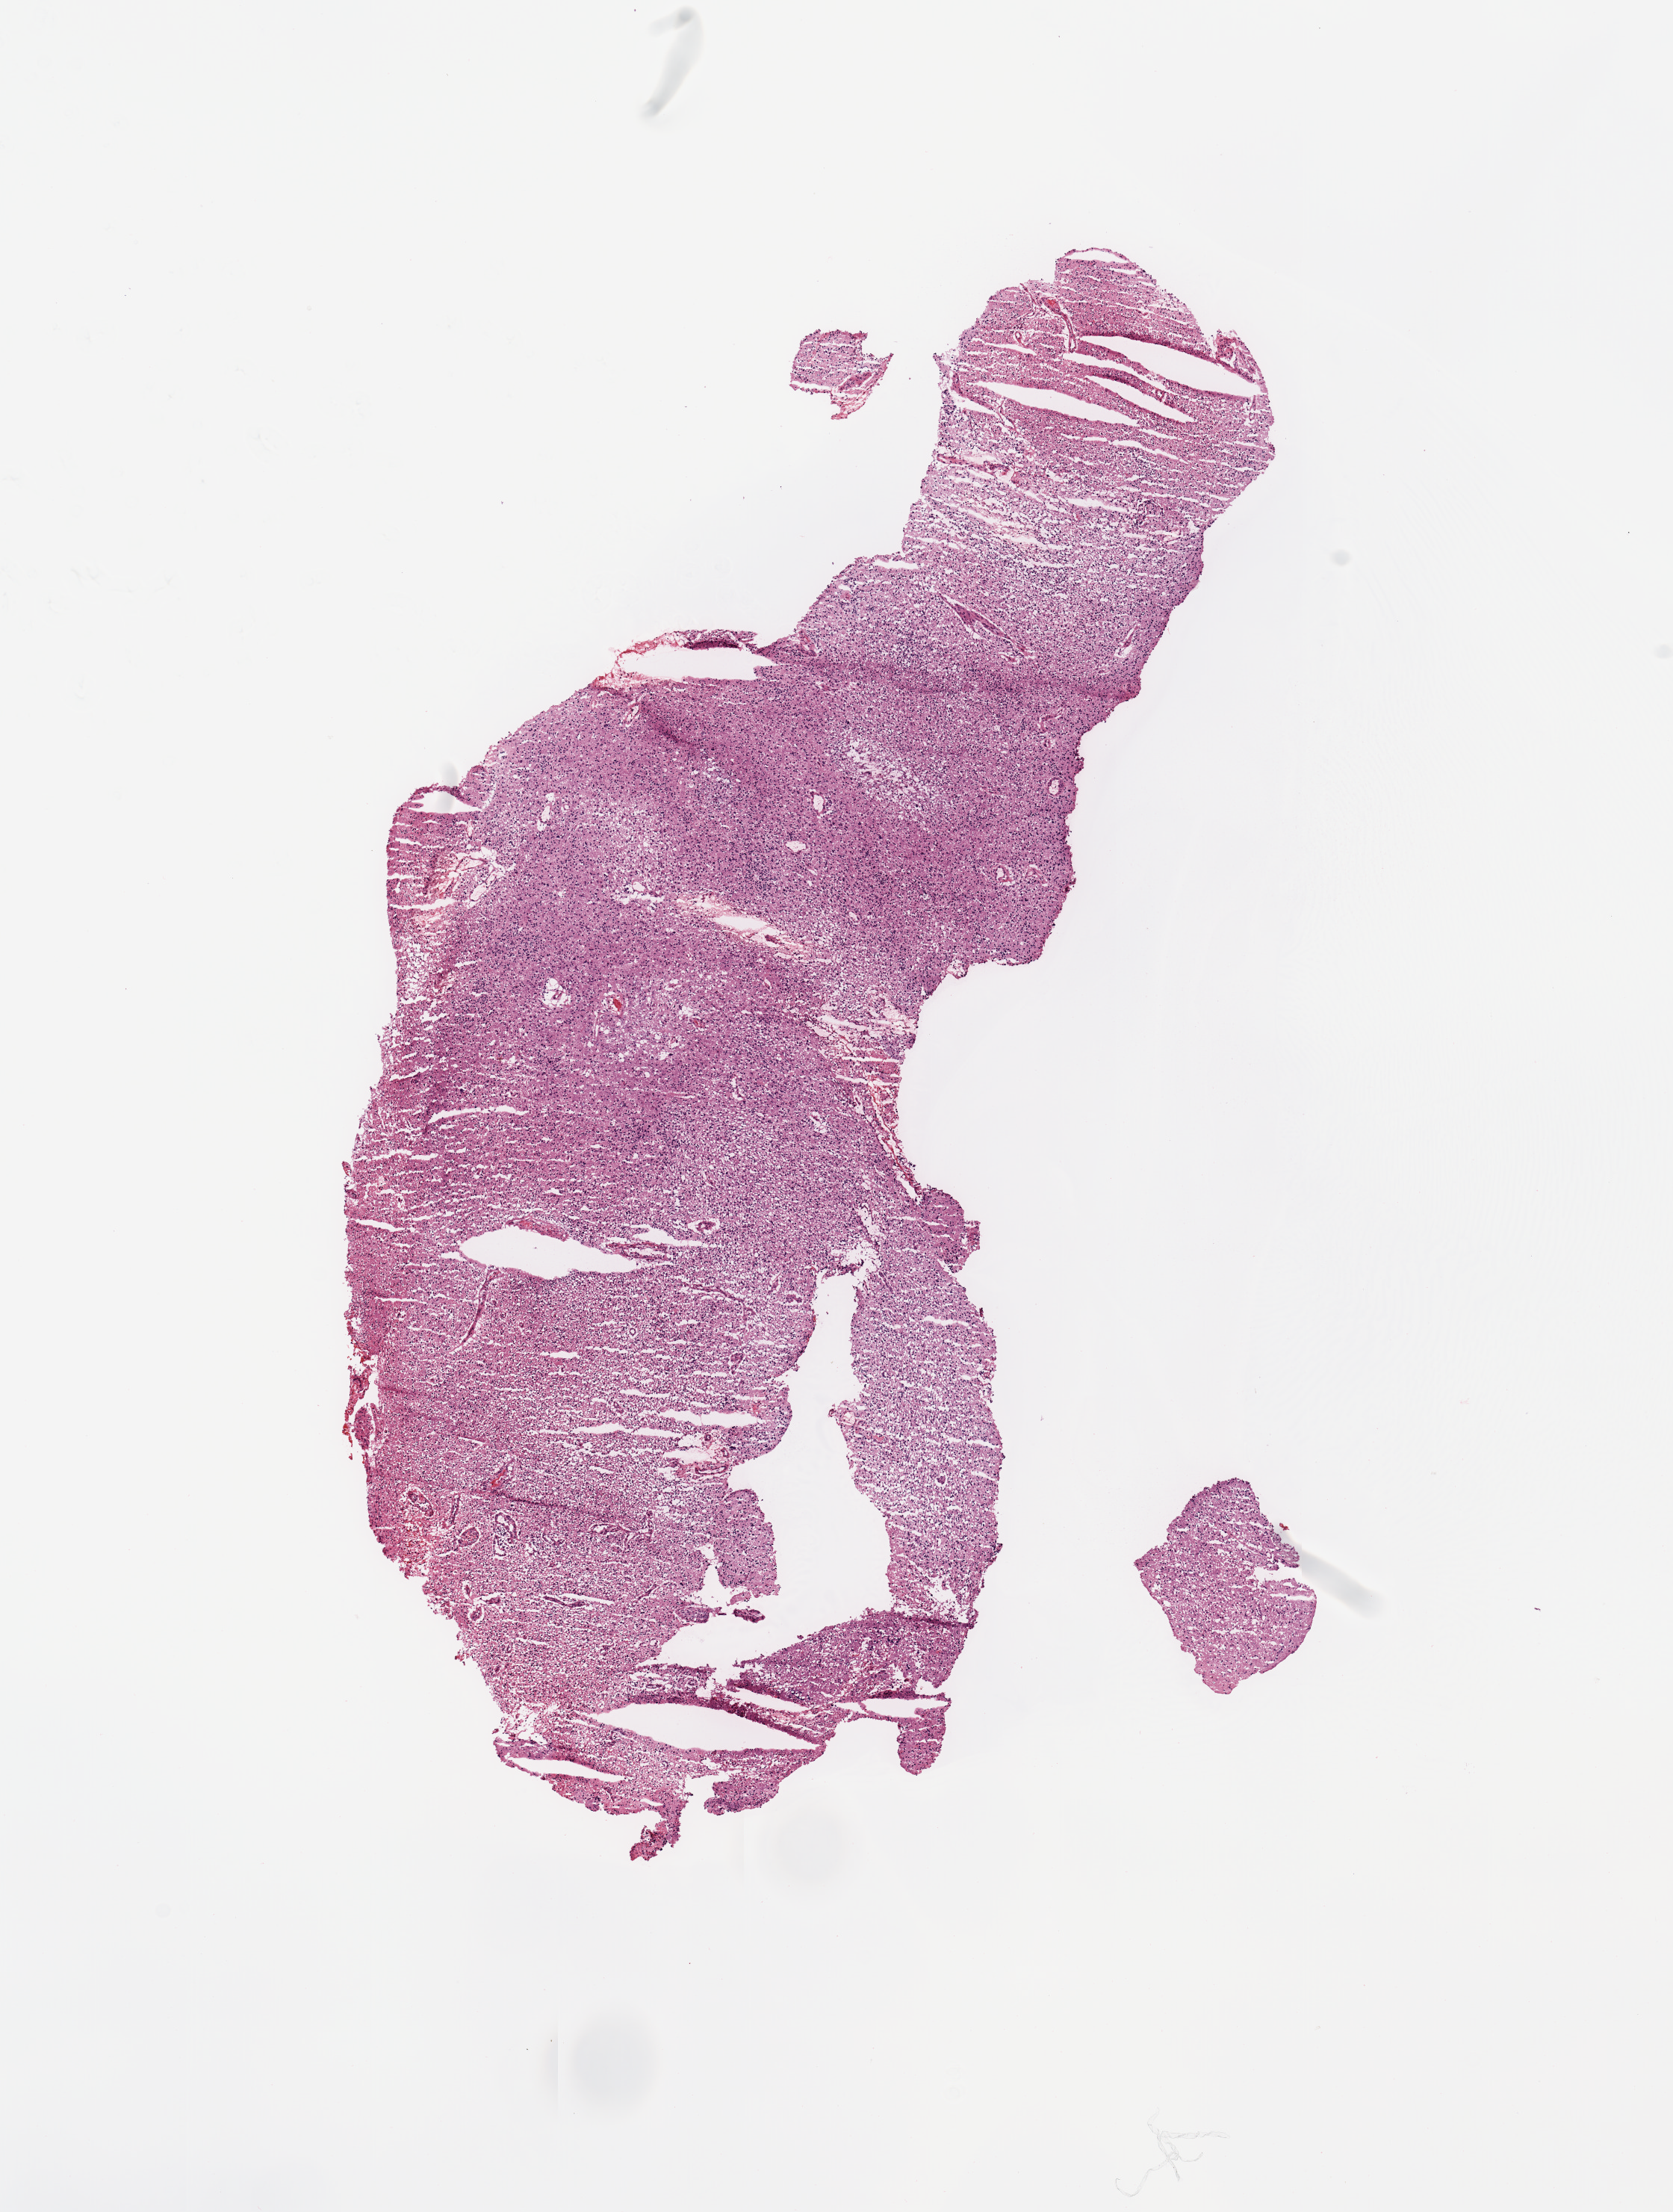
Digitized H&E tissue section (whole slide), low-resolution overview of the scanned area, about 8.9 x 11.7 mm (slide scanned at 20x); tumour tissue sample, brain. Patient: male, age 62 years.
• primary tumour site (as recorded): occipital lobe
• patient diagnosis (cohort enrolment): glioblastoma multiforme (brain)